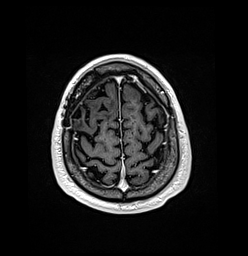
Brain MRI from a brain-tumour surgery series, one axial slice. Position 29 of 176 along the scan axis. T1-weighted post-contrast. 248 × 256 image matrix. Case-level facts recorded for this patient, not image findings: histopathology: Oligodendroglioma; WHO grade: 3; IDH mutation: yes; tumour location: Right Frontal.
Annotated regions visible in this slice (outlined manually by an expert reader):
- previous resection cavity: box from (x=72, y=105) to (x=83, y=125) px